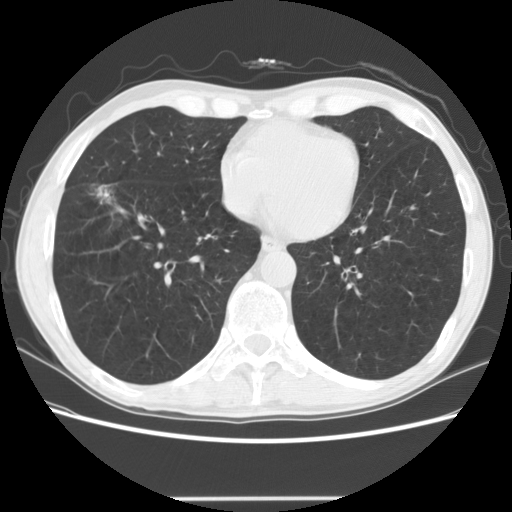
Axial slice from a low-dose chest CT screening exam, baseline annual screen, lung window (W 1500 / L -600 HU), 2.5 mm slice thickness, standard (soft-tissue) reconstruction kernel (STANDARD). Male participant, aged 69 years at enrolment.
- Lesion marked by an expert reader, bounding box (x1, y1, x2, y2) in pixels: (70, 168, 133, 222).
- Screening reader's record for this exam (one nodule recorded; not confirmed to be the boxed lesion): non-calcified nodule or mass ≥4 mm, right middle lobe, 20 × 14 mm, spiculated (stellate) margins, mixed attenuation.
- Official screen result: positive, change unspecified: nodule(s) >= 4 mm or enlarging nodule(s), mass(es), or other non-specific abnormalities suspicious for lung cancer.
- Later outcome: lung cancer diagnosed 86 days after this screen — squamous cell carcinoma, NOS, right middle lobe, poorly differentiated (G3), stage IA (AJCC 6th edition), 15 mm at pathology.